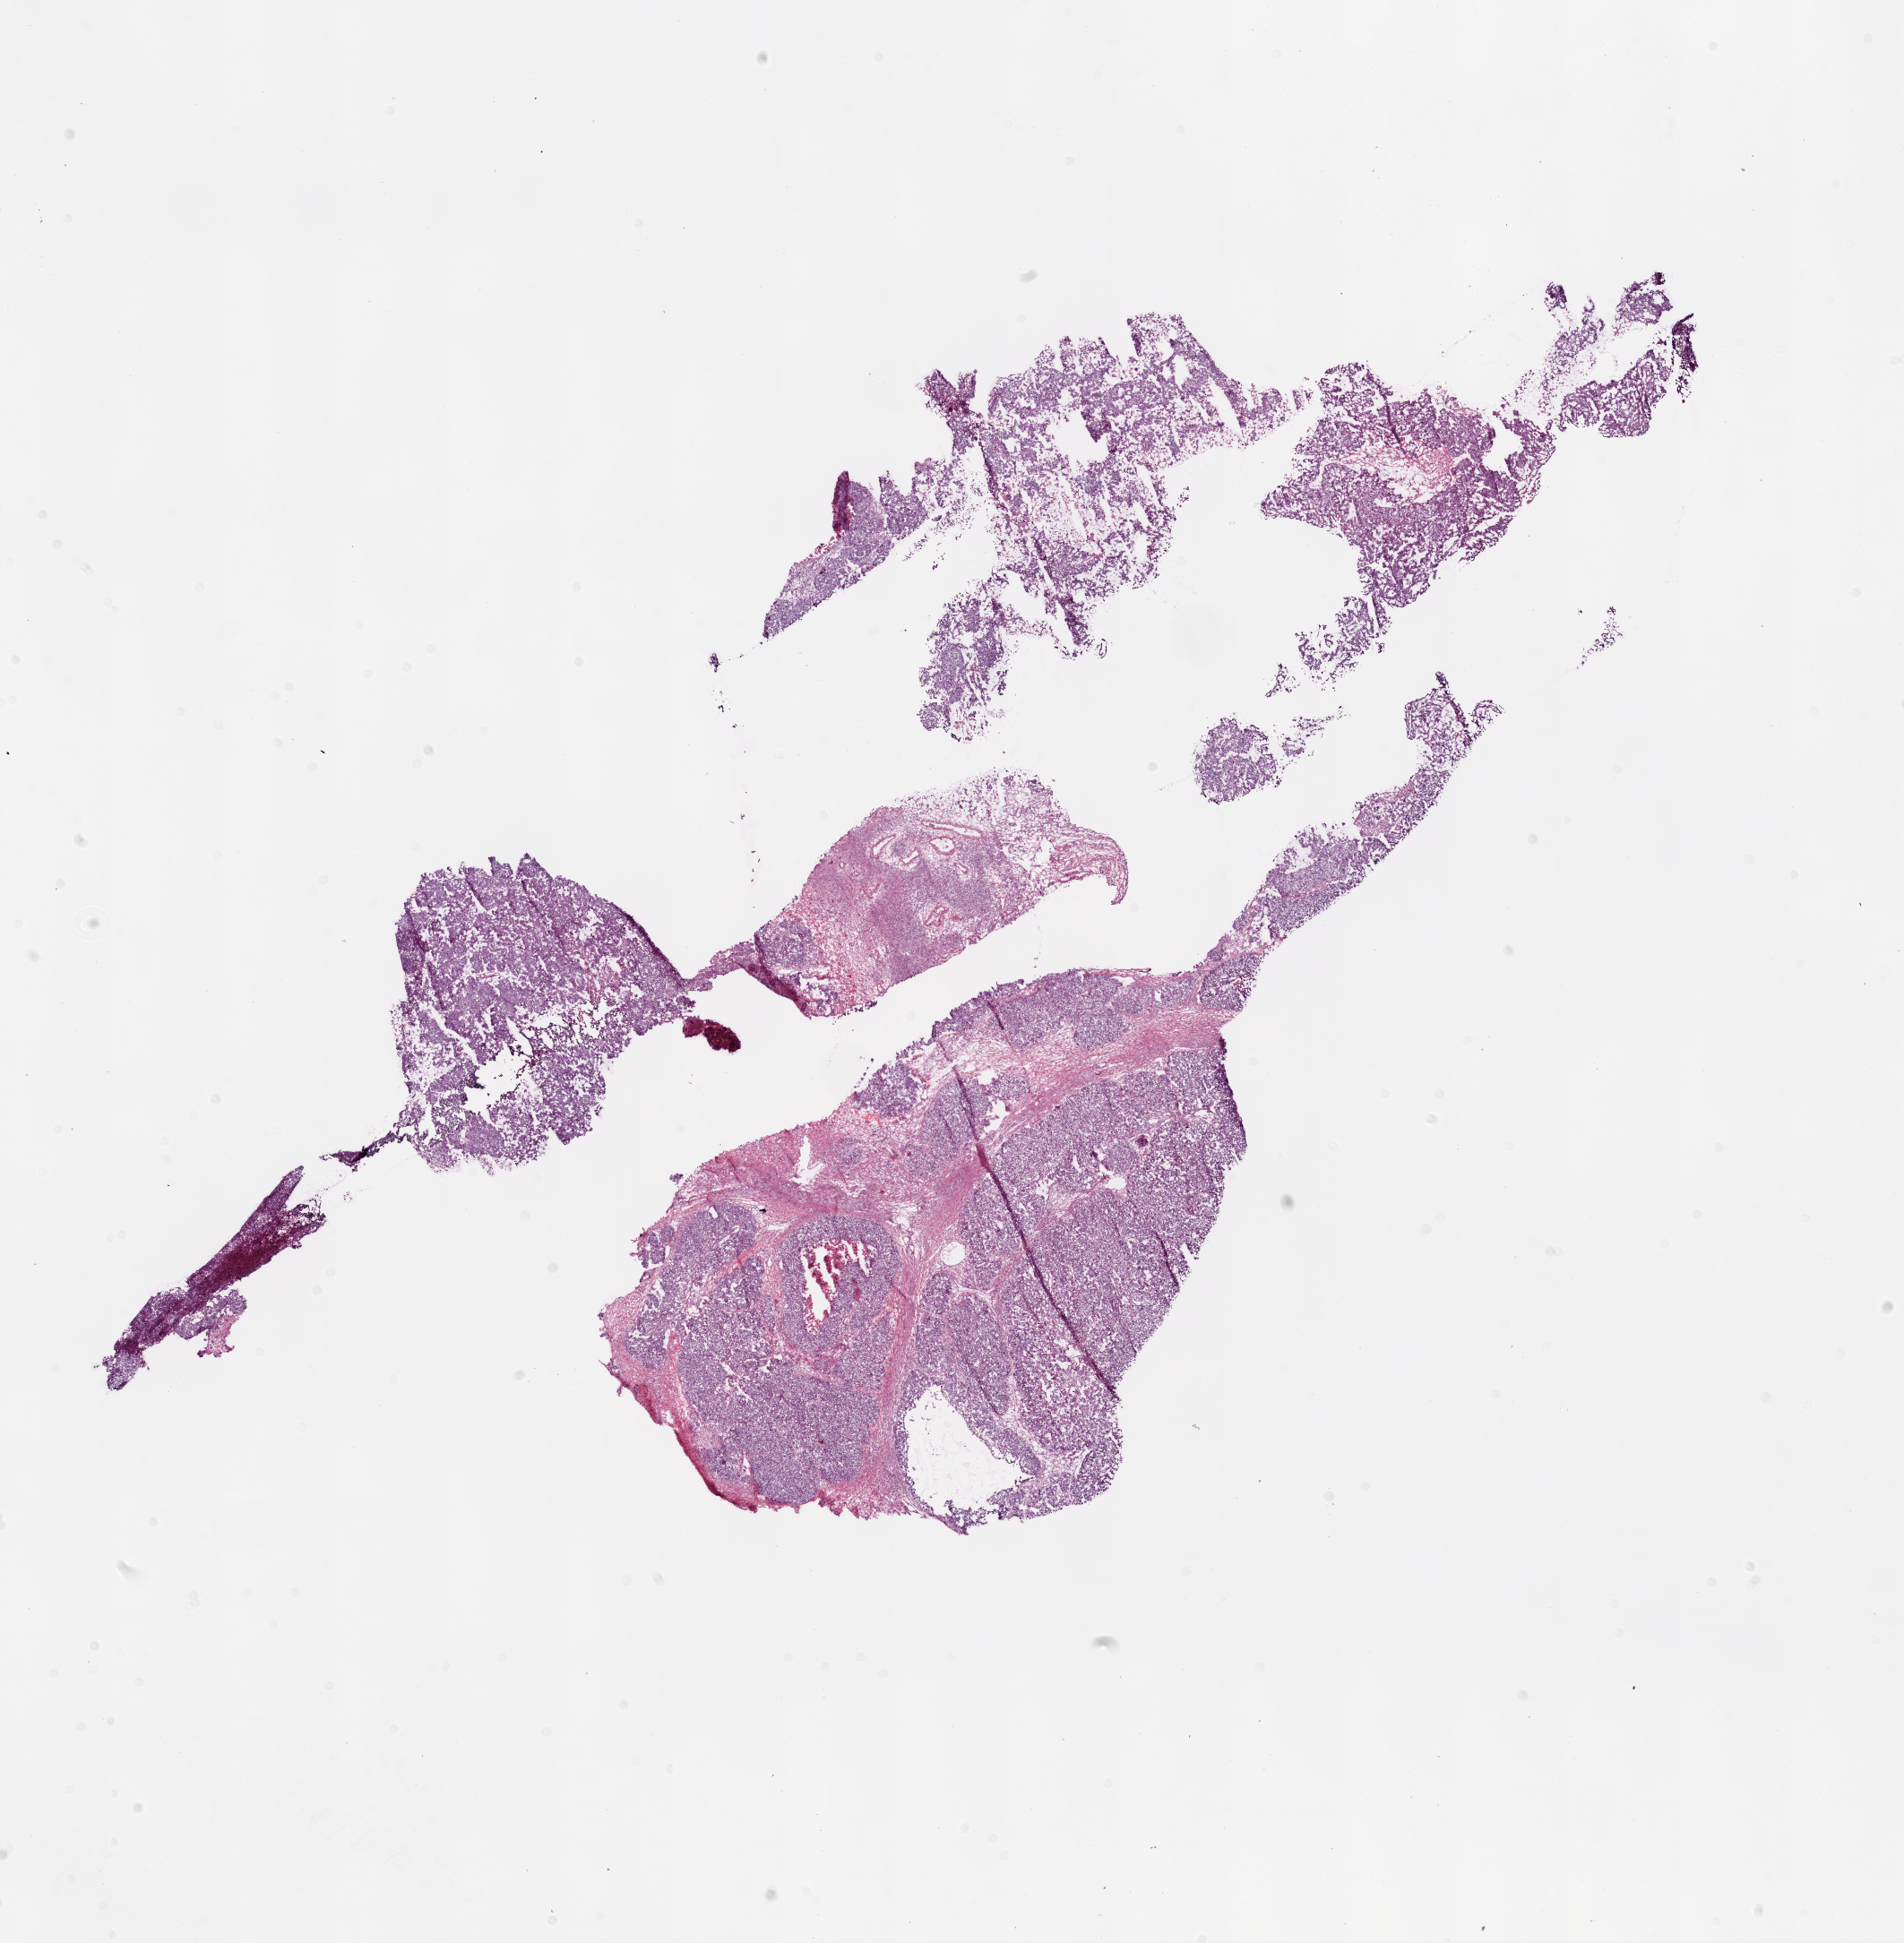
H&E-stained whole-slide image — whole scanned area (about 17.1 x 17.4 mm, from a 20x scan) shown as a low-resolution overview; frozen section from the bottom of the tissue portion; primary tumour sample from the ovary. Female patient; age at initial diagnosis 46 years.
Histologic diagnosis: Serous cystadenocarcinoma, NOS.